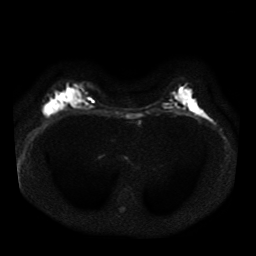
Breast MRI, one axial slice. Position 23 of 41 along the scan axis. Diffusion-weighted series; image 2 of 4 stored at this slice position (different b-values; order by instance number). 1.5 T. 5 mm slice thickness. 256 × 256 image matrix, field of view 330 × 330 mm. Female patient.
Outlined on this slice (manually delineated by an expert):
- tumour on diffusion-weighted imaging: bounding box <42,95,63,113> (left, top, right, bottom; pixels)